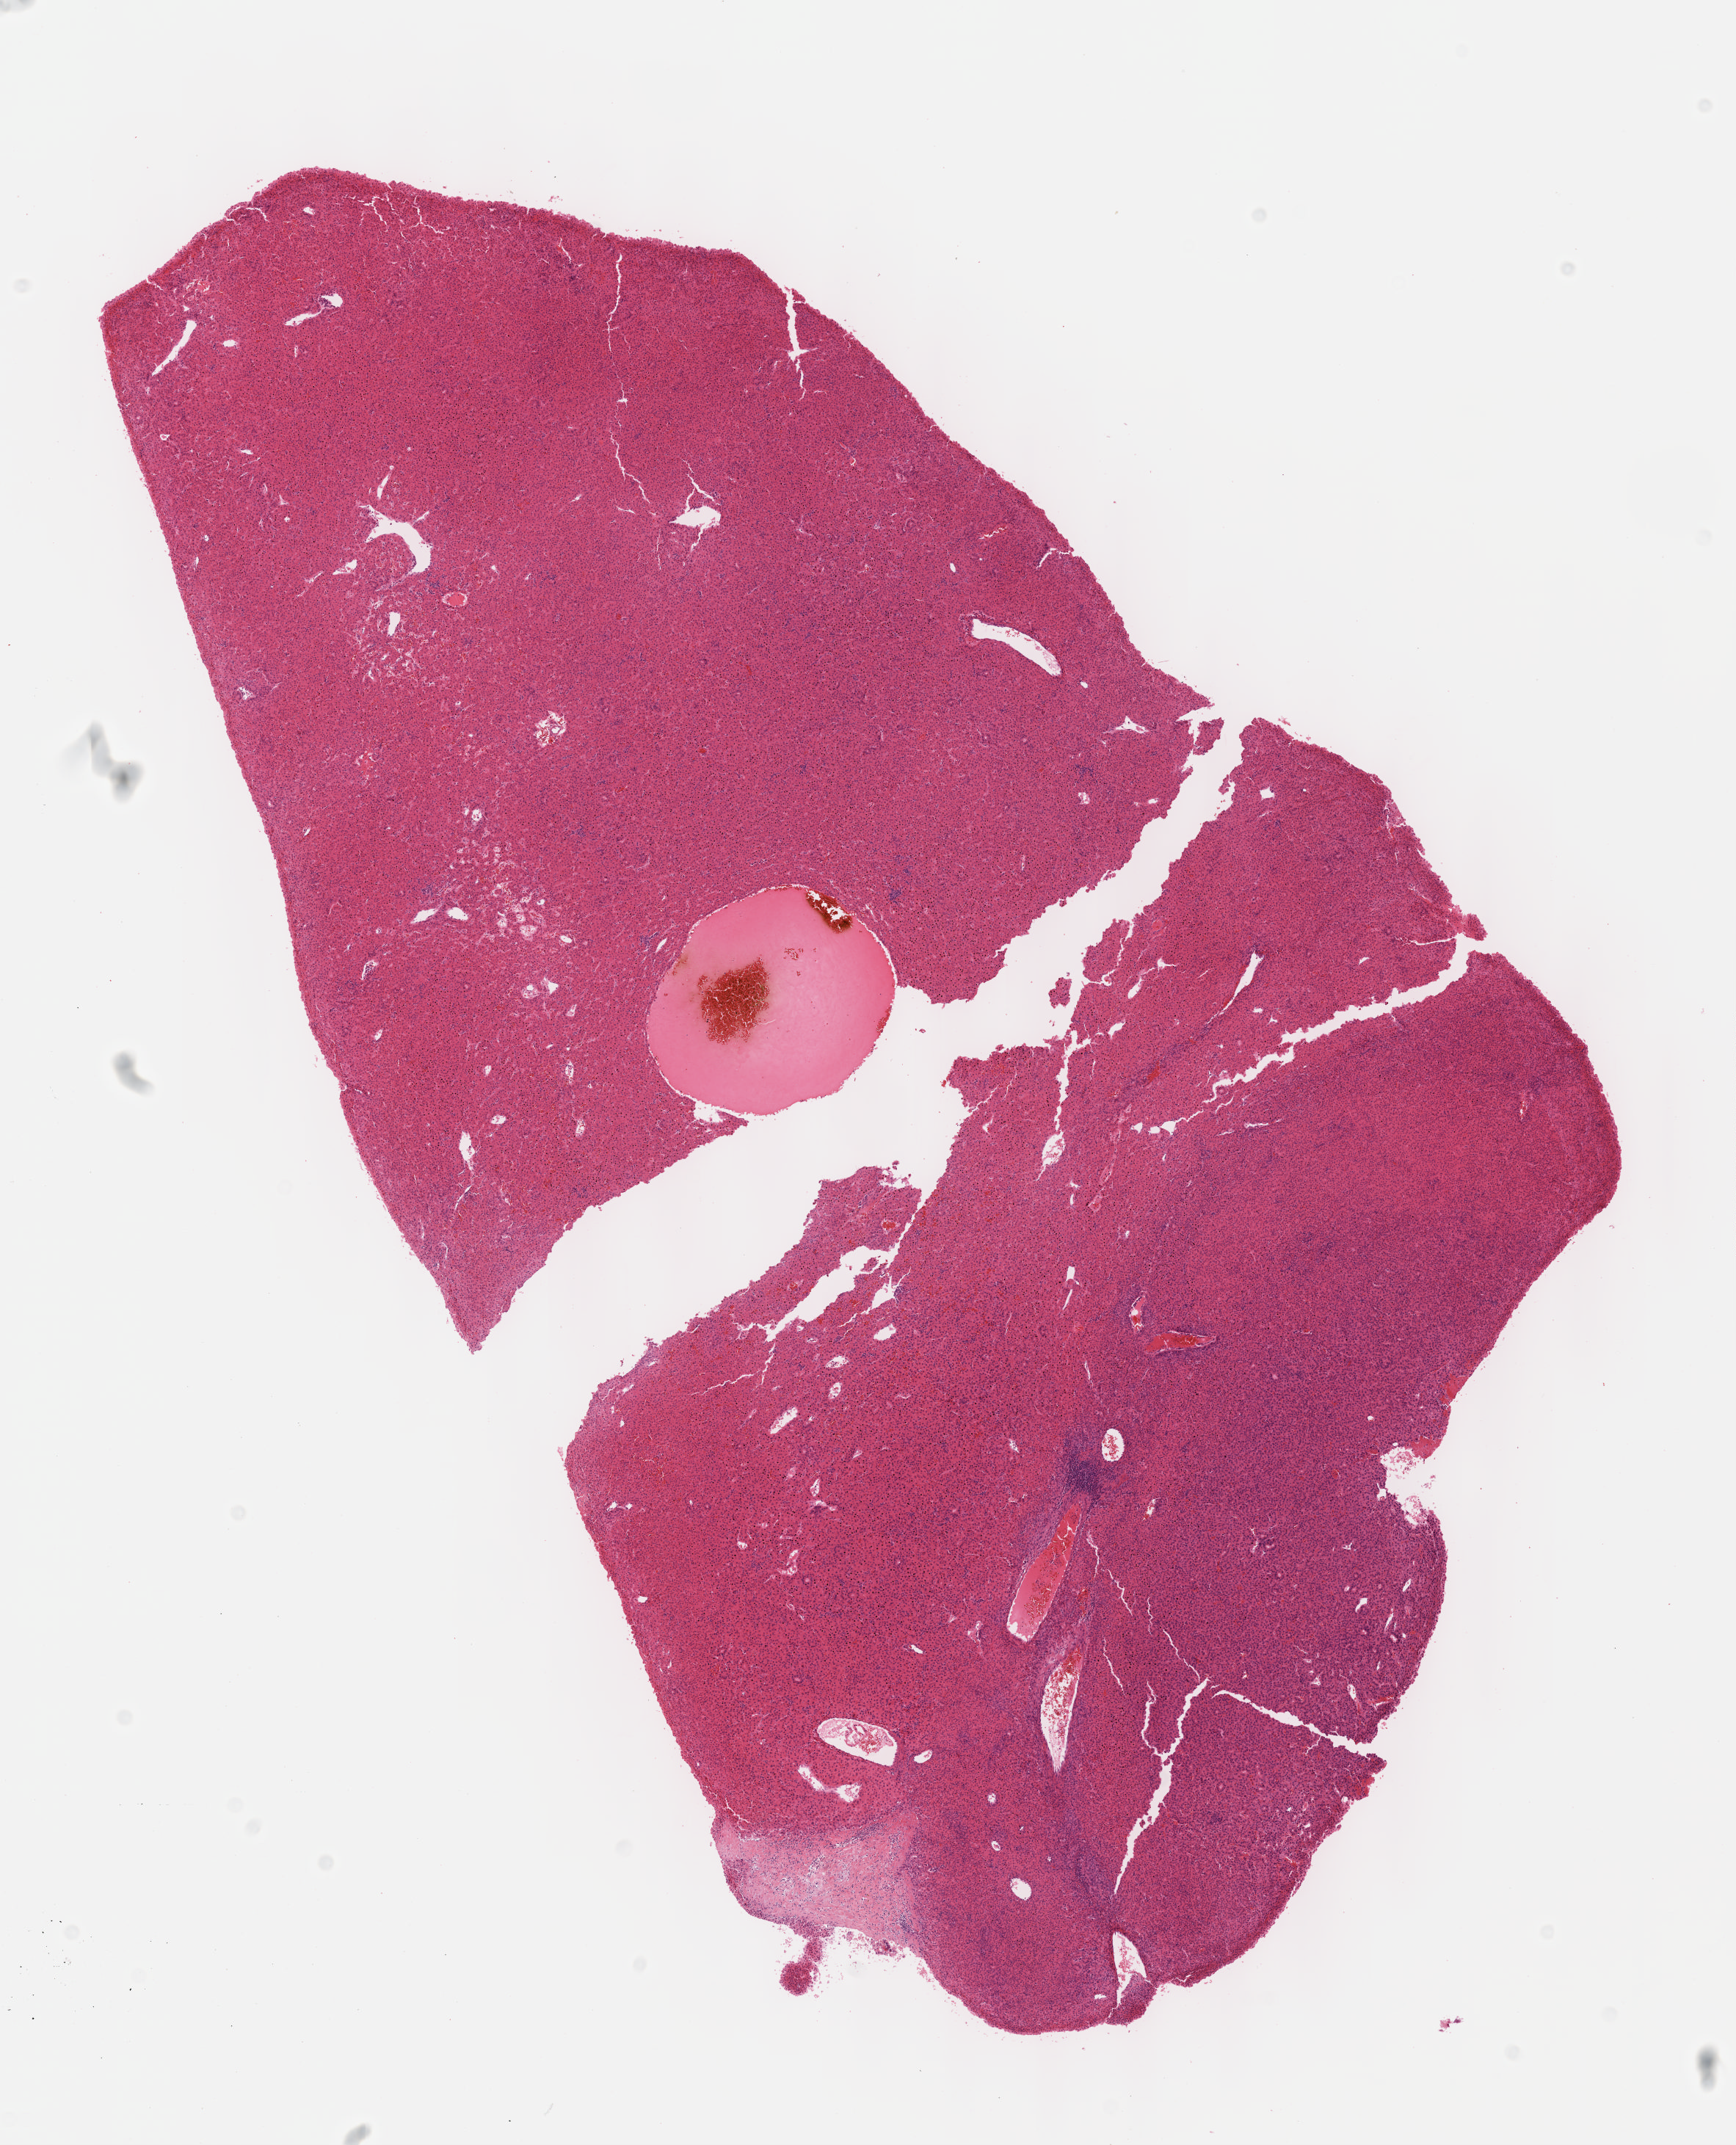
Whole-slide histology image, H&E-stained — whole scanned area (about 9.6 x 11.8 mm, acquisition: 40x scan) shown as a low-resolution overview. FFPE section. Liver, primary tumour sample. Male, age 63 years at initial diagnosis. Histologic grade: G2 (moderately differentiated).
TNM: T1 N0 M0. Histologic diagnosis: Hepatocellular carcinoma, NOS. AJCC pathologic stage: I (7th edition).